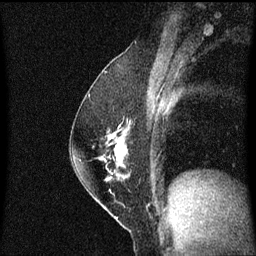
Breast MRI (dynamic contrast-enhanced), one sagittal slice. Slice 34 of 60 in the series (ordered by position). Dynamic contrast-enhanced series, image 2 of 3 at this slice position (ordered by acquisition). 1.5 T. TE 4.2 ms, TR 8.4 ms. 2 mm slice thickness. 256 × 256 image matrix. Patient: female, 52 years. From the clinical record (not read from this slice): setting: breast cancer imaged before/during neoadjuvant chemotherapy; receptor status: HER2-positive.
Outlined on this slice (semi-automatic segmentation, software-assisted and operator-edited):
- analysis volume of interest (the breast-tissue region the enhancement analysis was run in; not a lesion): bounding box <71,118,132,187> (left, top, right, bottom; pixels)
- tumour enhancement mask (voxels above the 70 % enhancement threshold inside the analysis volume of interest): <109,136,127,157>